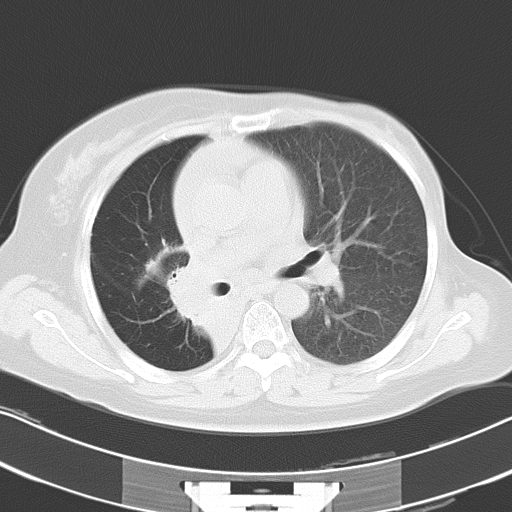
Chest CT, one axial slice. Slice 18 of 30 in the series (ordered by position). Reconstruction kernel B70f. 120 kVp. Lung window (W 1500 / L -600 HU). 512 × 512 image matrix, field of view 331 × 331 mm. Patient: female, 53 years. From the clinical record (not read from this slice): clinical TNM (as recorded): T2b N1 M0.
Outlined on this slice (rectangle marked by the reading radiologist):
- lung tumour (recorded histology: adenocarcinoma): bounding box (x1, y1, x2, y2) in pixels: (167, 263, 231, 341)